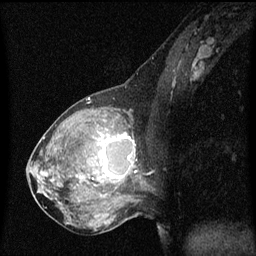
Breast MRI (dynamic contrast-enhanced), one sagittal slice. Position 28 of 60 along the scan axis. Dynamic contrast-enhanced series, image 2 of 3 at this slice position (ordered by acquisition). 1.5 T. TE 4.2 ms, TR 8 ms. 2 mm slice thickness. 256 × 256 image matrix, field of view 200 × 200 mm. Female patient, age 50 years.
Outlined on this slice (semi-automatic segmentation, software-assisted and operator-edited):
- analysis volume of interest (the breast-tissue region the enhancement analysis was run in; not a lesion): box from (x=91, y=126) to (x=139, y=189) px
- tumour enhancement mask (voxels above the 70 % enhancement threshold inside the analysis volume of interest): (x=92, y=134)–(x=135, y=181)